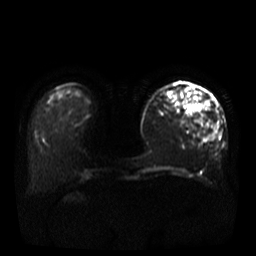
Breast MRI, one axial slice; position 10 of 37 along the scan axis; diffusion-weighted series; image 2 of 4 stored at this slice position (different b-values; order by instance number); 3 T; 5 mm slice thickness; 256 × 256 image matrix, field of view 380 × 380 mm. Female patient.
Structures marked on this image (manually delineated by an expert):
- tumour on diffusion-weighted imaging: bounding box <199,116,218,140> (left, top, right, bottom; pixels)